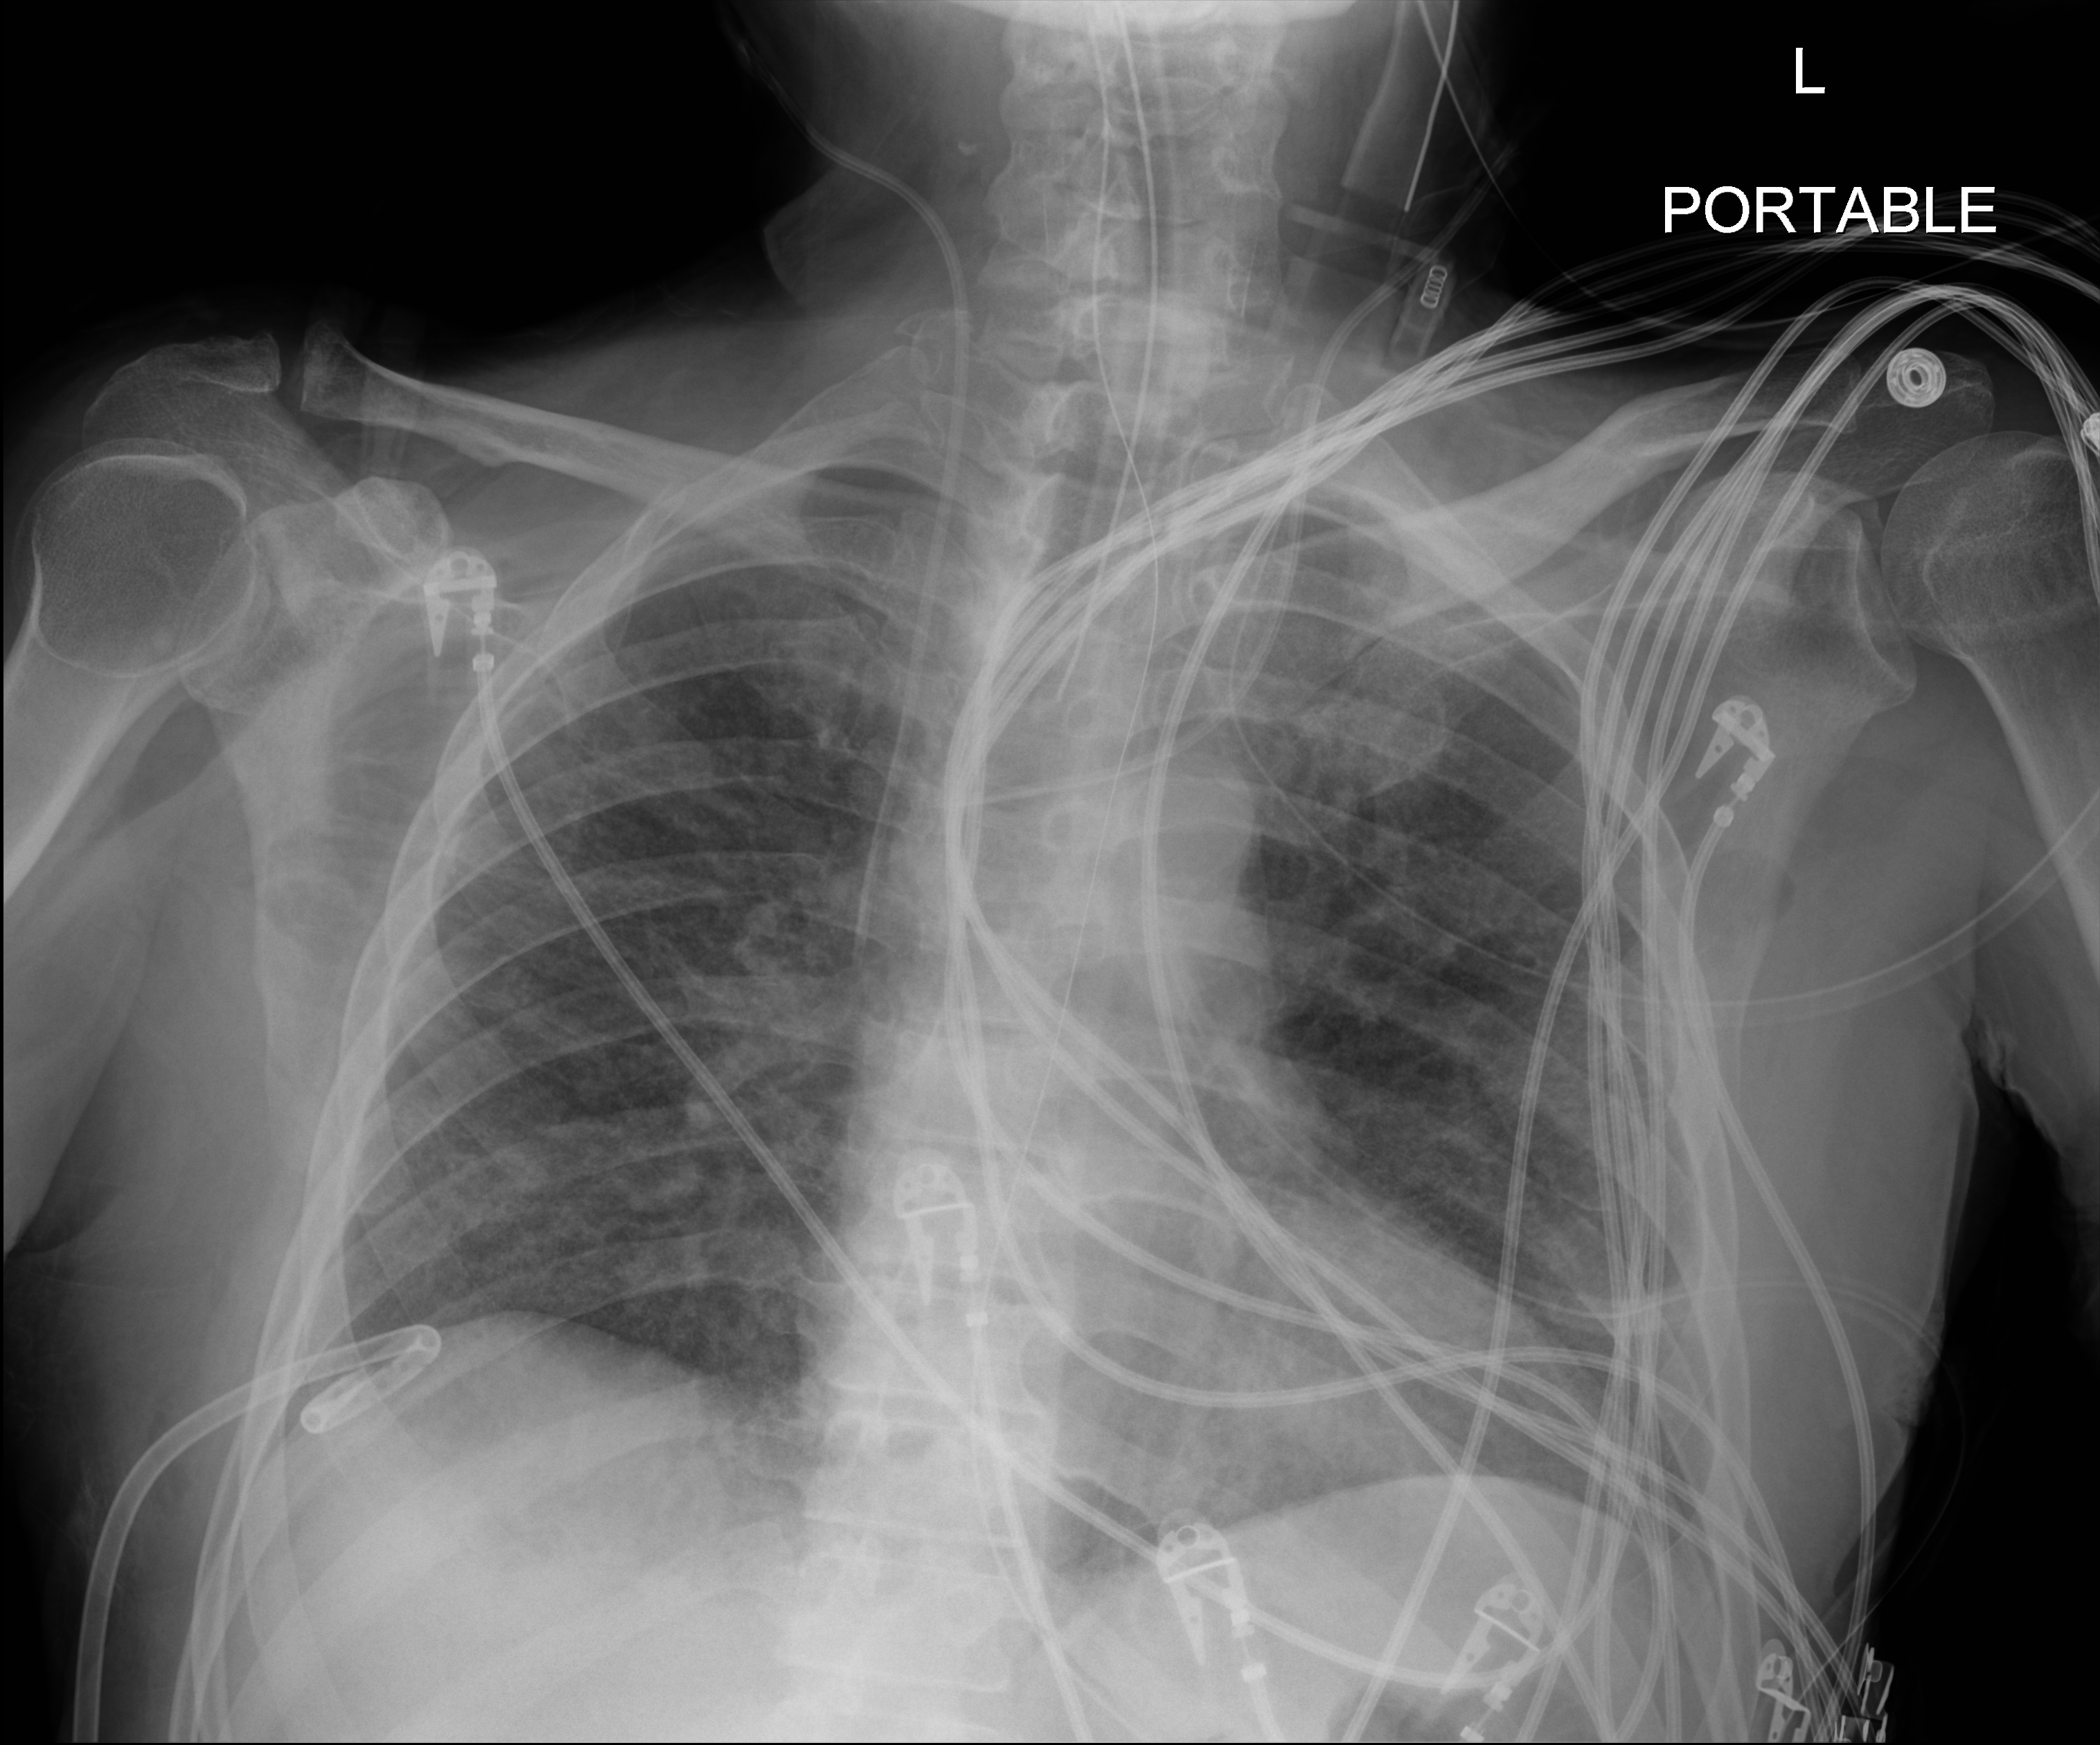
Chest X-ray (portable); anteroposterior (AP) projection. Male patient hospitalised with COVID-19, age 18–59 years.
From the hospital-stay record, not from the radiograph (when in the stay this image was taken is not recorded): length of hospital stay: 77 days; mechanically ventilated during this hospital stay: yes.